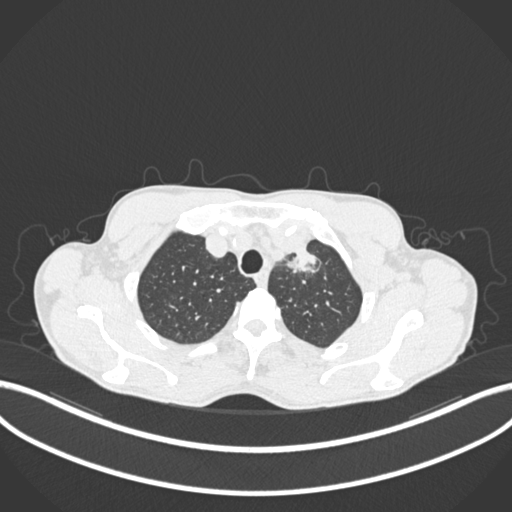
Chest CT, one axial slice. Slice 176 of 211 in the series (ordered by position). Lung window (W 1500 / L -600 HU). 1 mm slice thickness. 512 × 512 image matrix, field of view 400 × 400 mm. Male patient, age 58 years. Case-level facts recorded for this patient, not image findings: clinical TNM (as recorded): T1c N1 M0.
Annotated regions visible in this slice (bounding box drawn by a radiologist):
- lung tumour (recorded histology: adenocarcinoma): bounding box <282,239,331,280> (left, top, right, bottom; pixels)